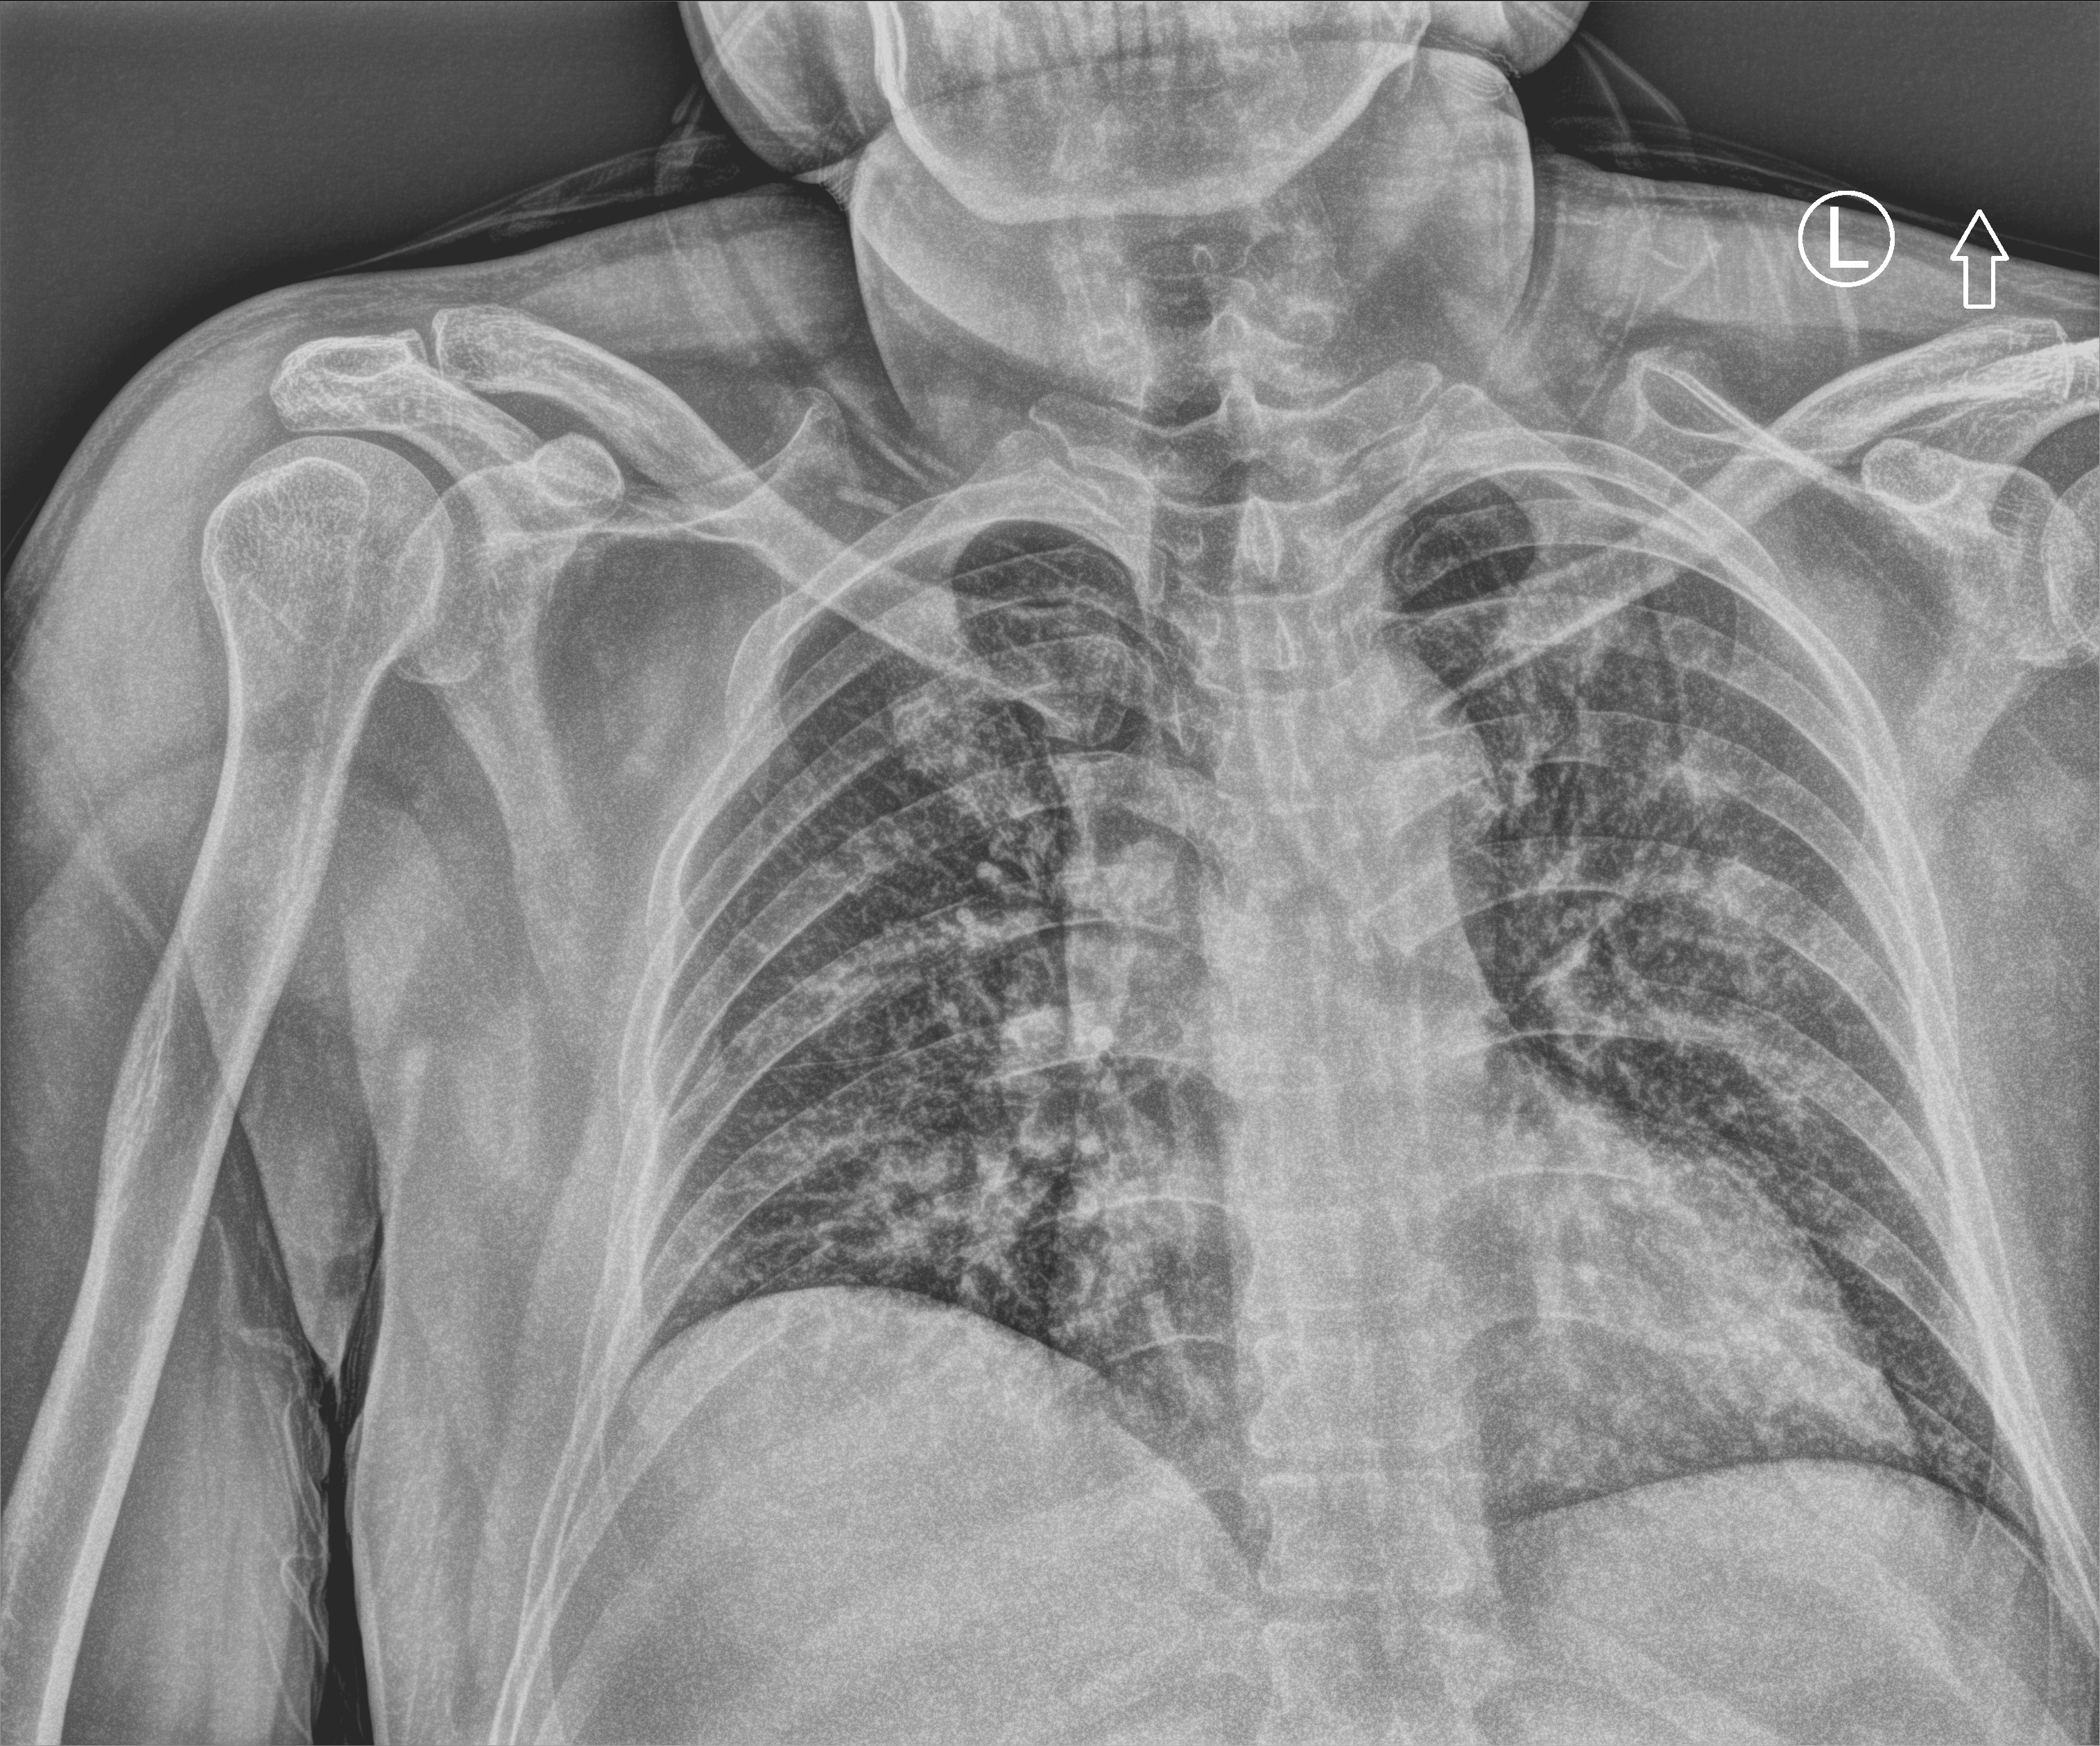
Portable chest radiograph. Patient hospitalised with COVID-19; male, aged 18–59 years.
From the hospital-stay record, not from the radiograph (when in the stay this image was taken is not recorded):
- admitted to intensive care during this hospital stay: no
- hypertension (admission record): no
- mechanically ventilated during this hospital stay: no